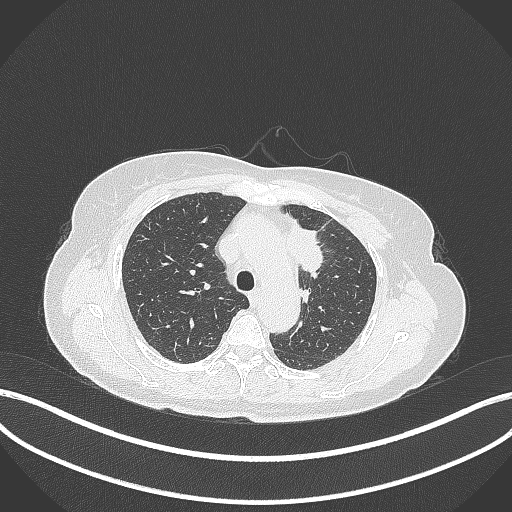
Chest CT, one axial slice; position 243 of 369 along the scan axis; 120 kVp; lung window (W 1500 / L -600 HU); 1 mm slice thickness; 512 × 512 image matrix. Female patient, age 65 years. Case-level facts recorded for this patient, not image findings: clinical TNM (as recorded): T2a N0 M0.
Outlined on this slice (rectangle marked by the reading radiologist):
- lung tumour (recorded histology: adenocarcinoma): bounding box (x1, y1, x2, y2) in pixels: (281, 216, 326, 279)